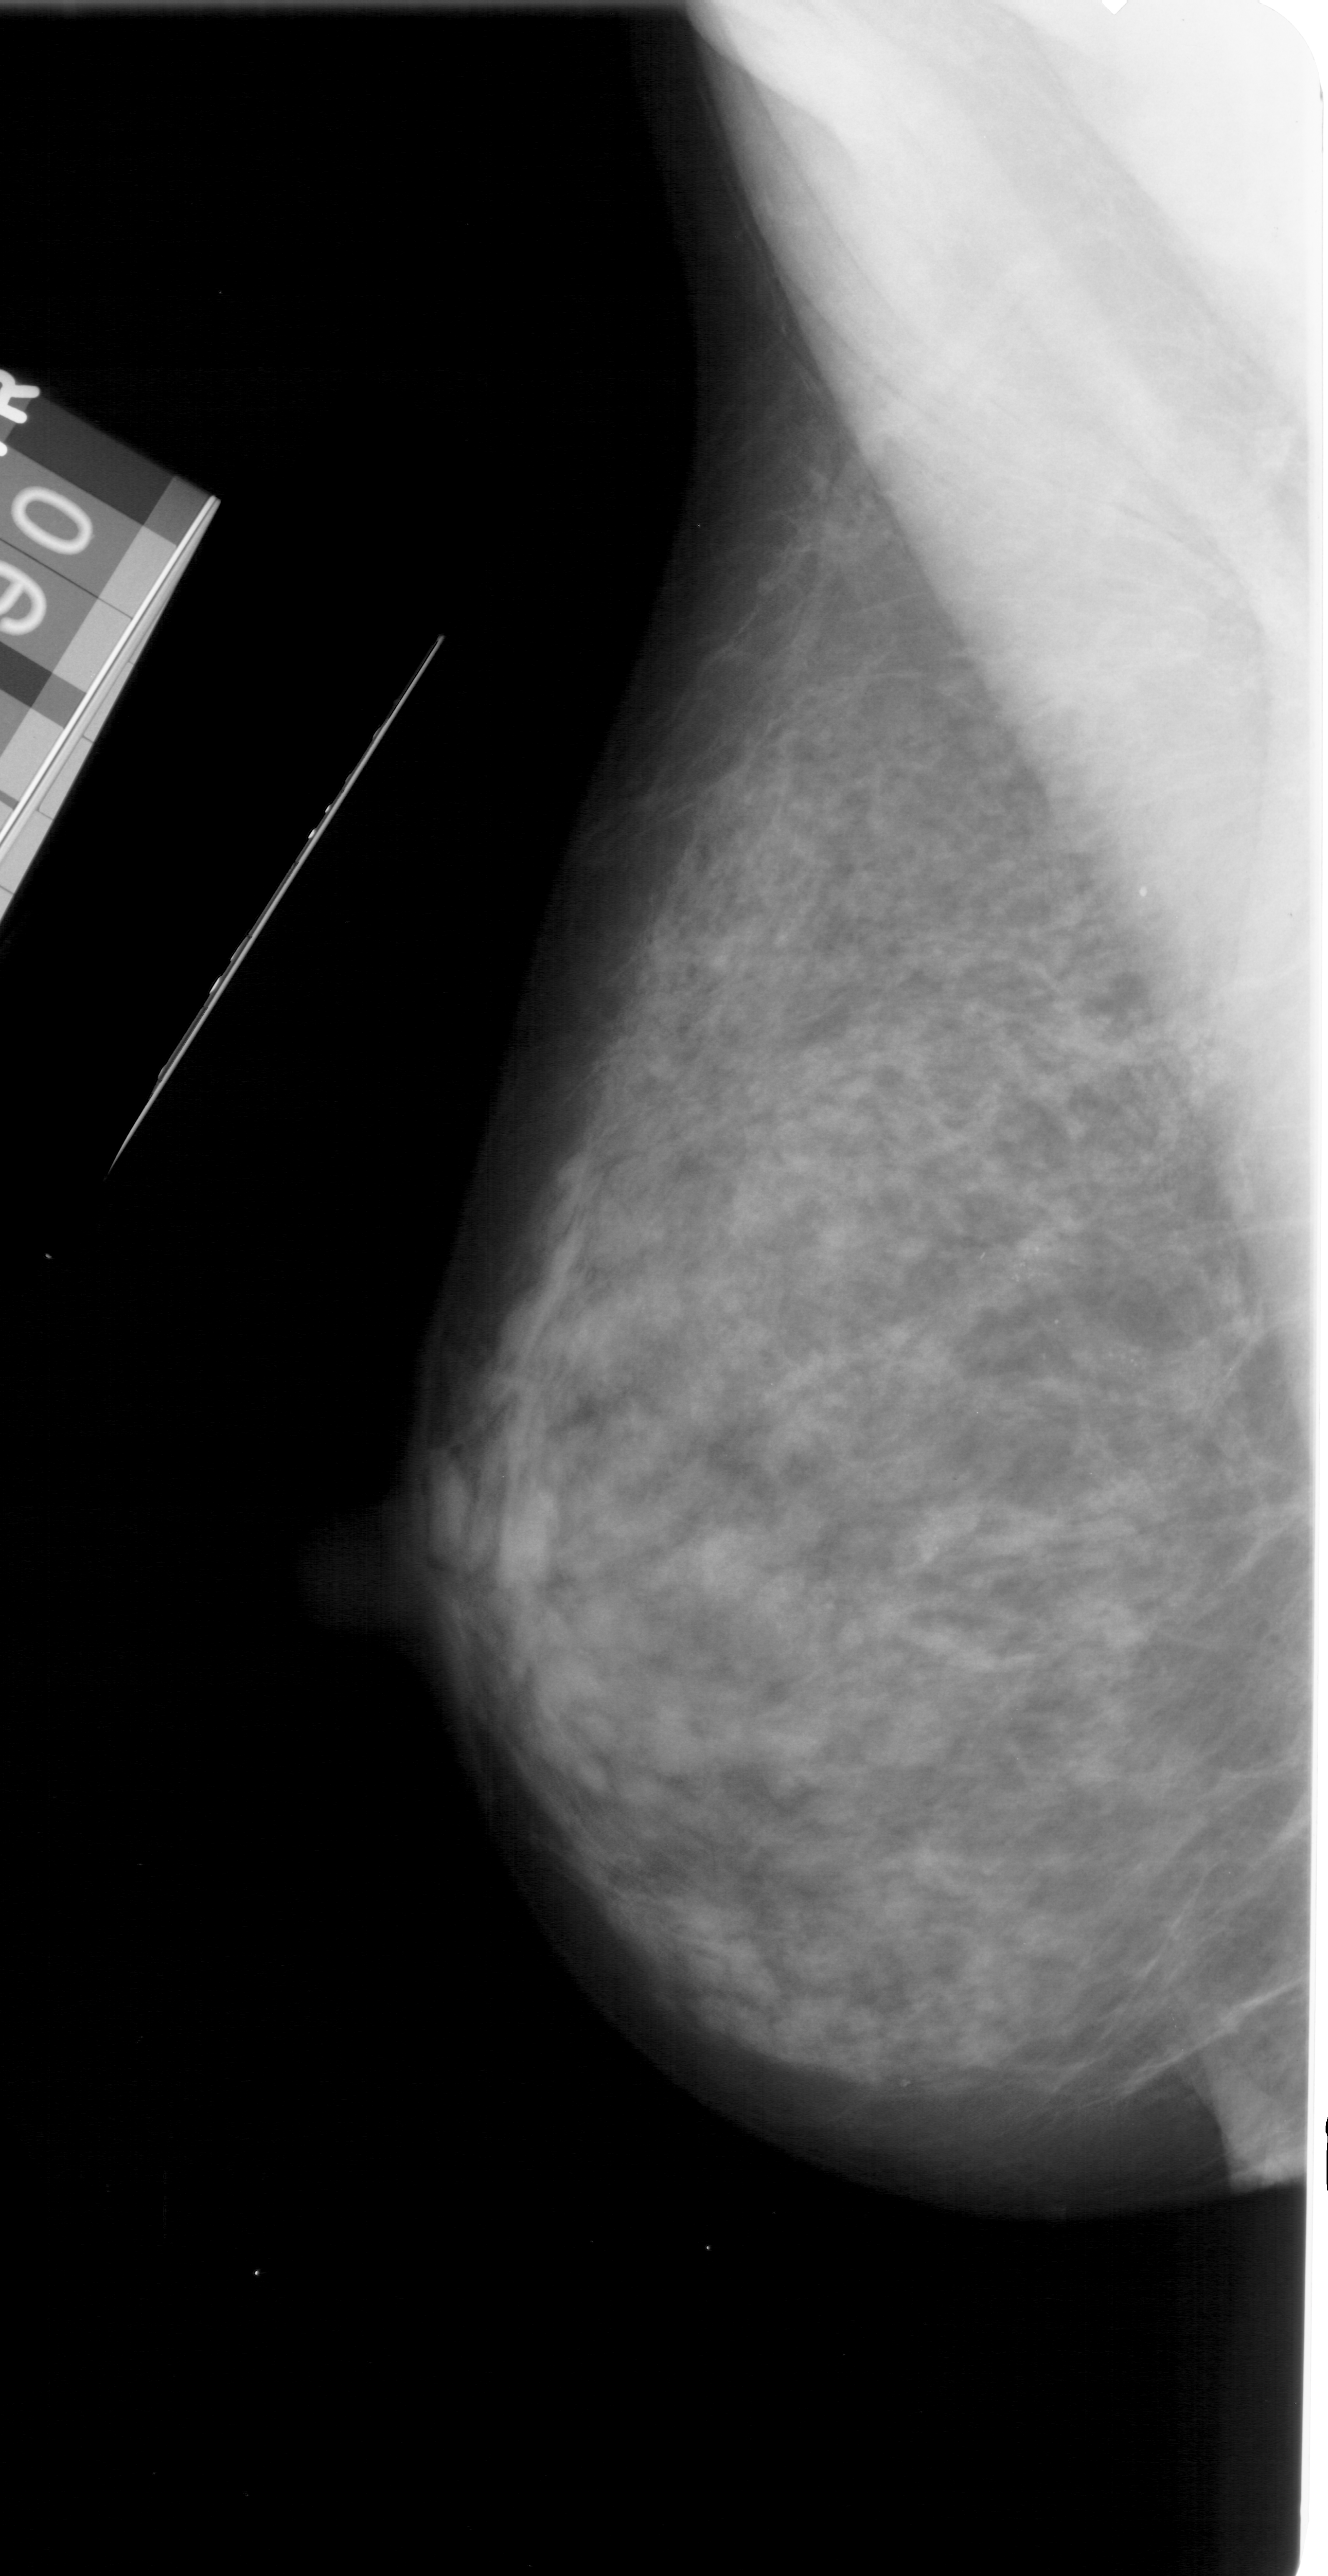
Mammogram (digitized film); left breast; mediolateral oblique (MLO) view; breast composition: heterogeneously dense (BI-RADS density category 3 of 4).
- Marked abnormality: calcifications, morphology pleomorphic, distribution segmental; BI-RADS assessment category 4; subtlety rating 3 on a 1 (subtle) to 5 (obvious) scale; pathology result (as recorded, not read from the image): malignant.